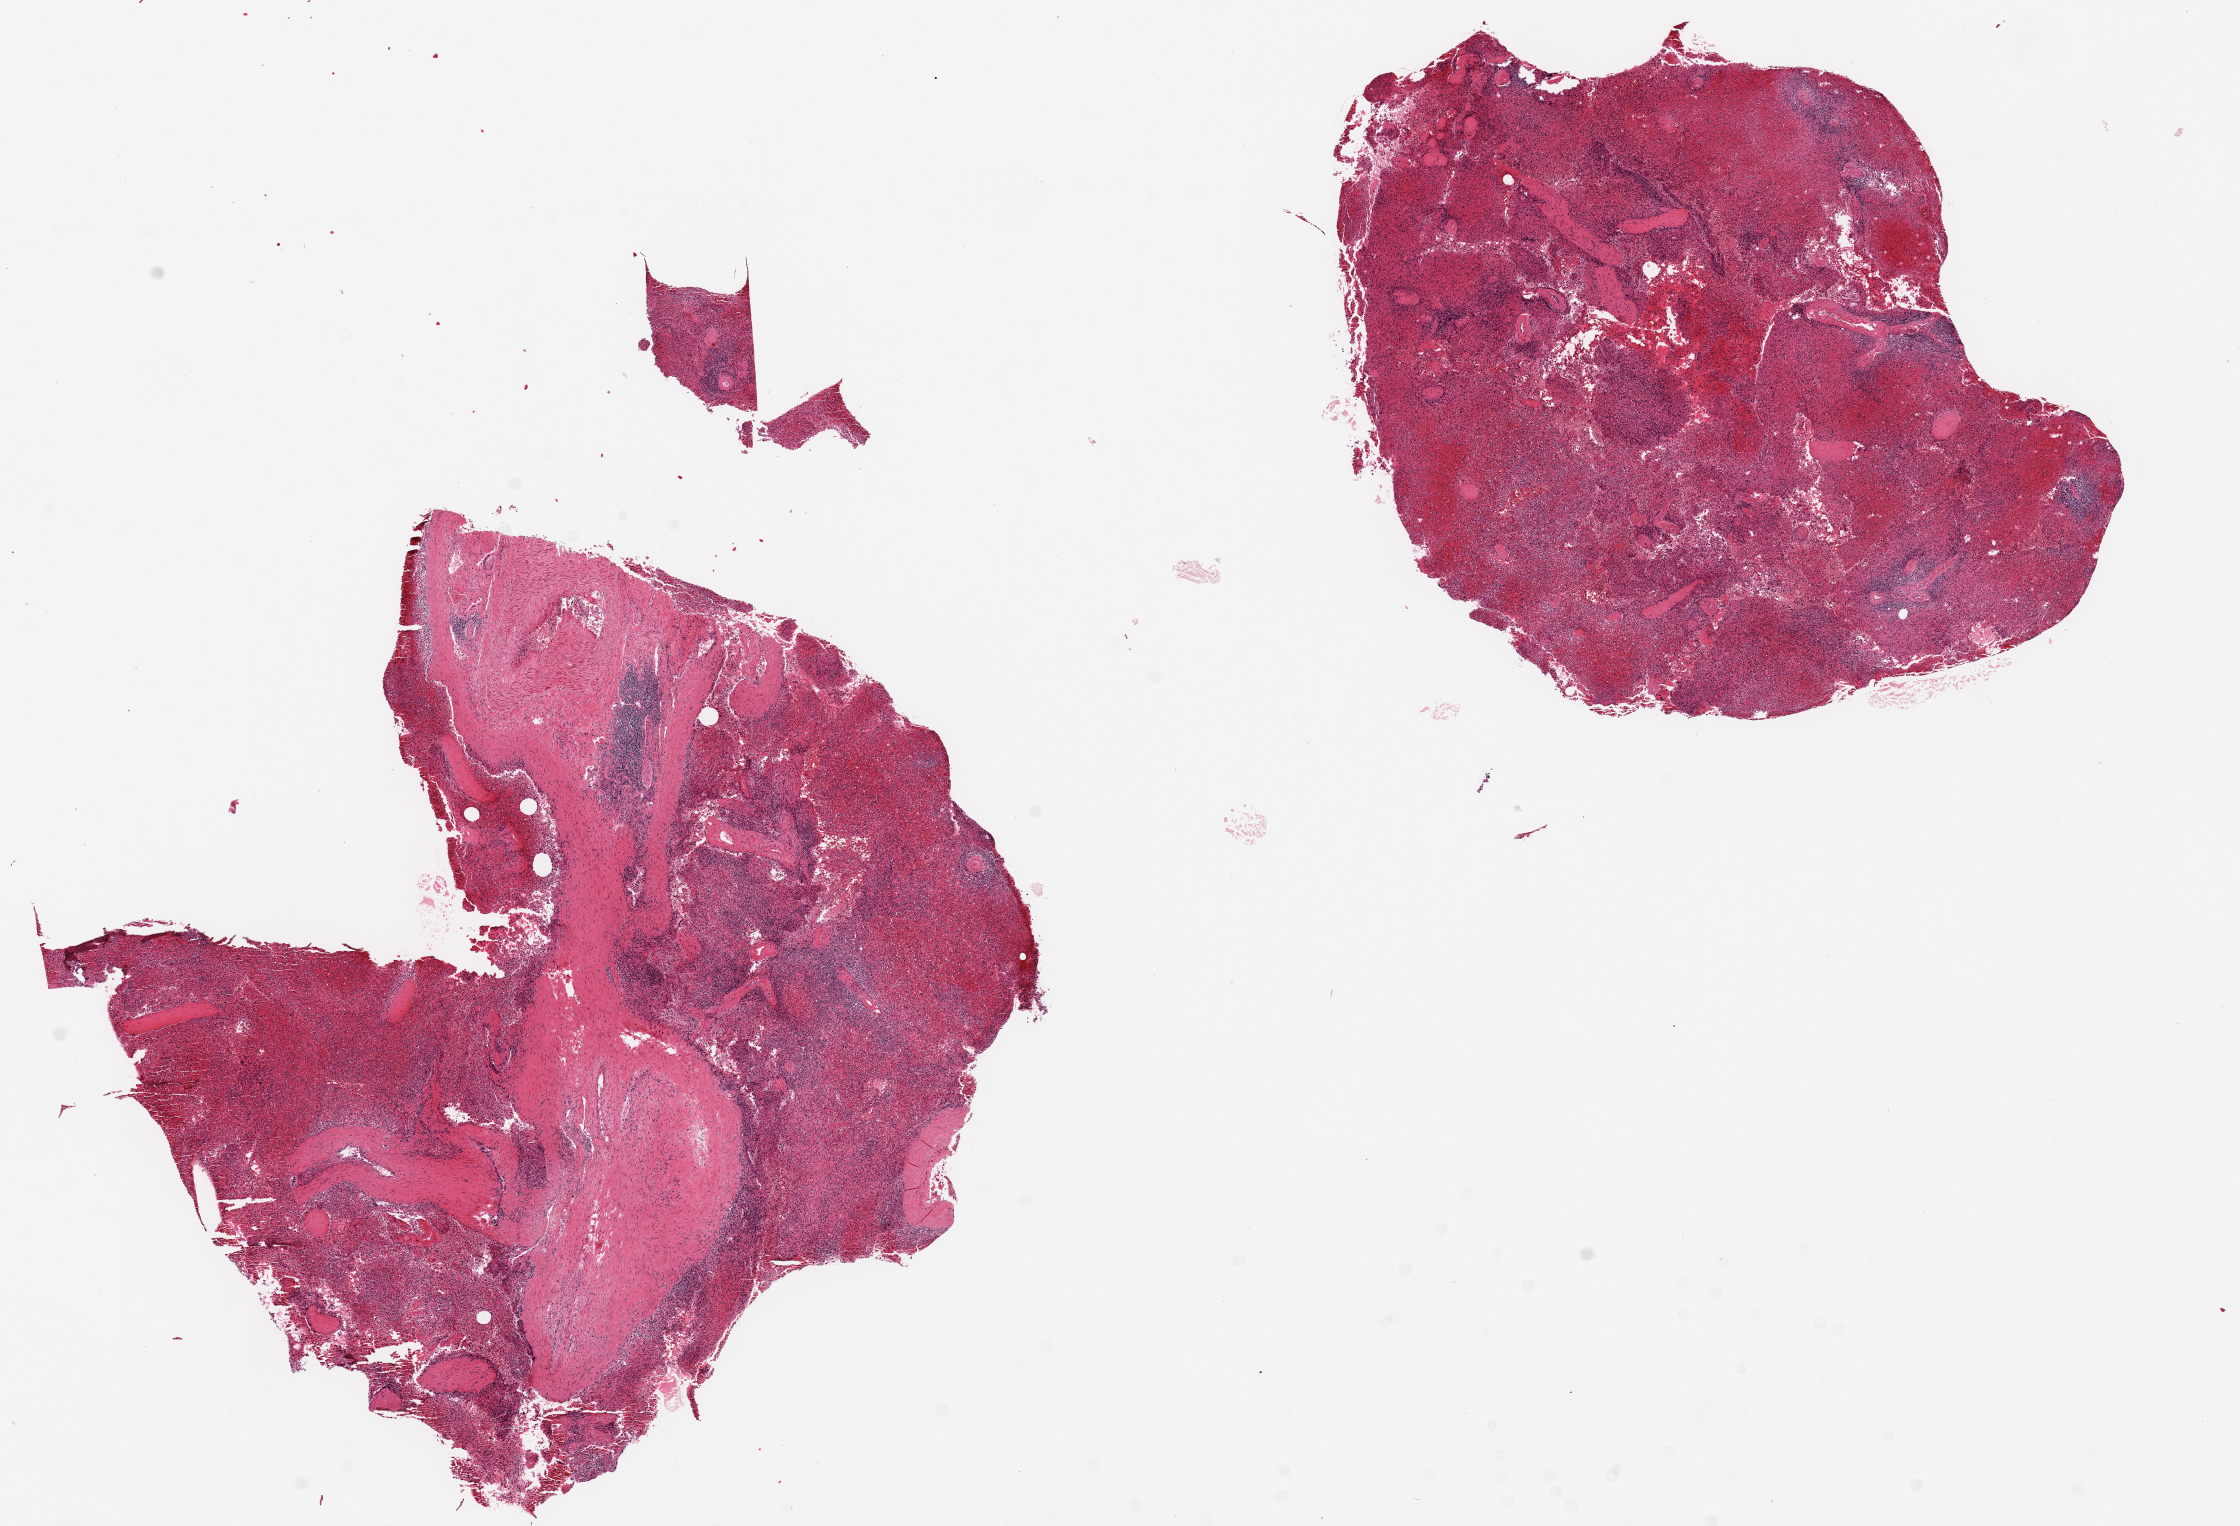
Digitized H&E-stained section, brightfield — low-resolution overview of the scanned area, about 17.7 x 12.1 mm (from a 20x scan), PAXgene-fixed paraffin-embedded (PFPE) section, section of spleen (target tissue), tissue donor sample.
Review note (as recorded): 2 pieces, 7x7 & 7x5mm; congested; large vessels at center of one piece (~40%).